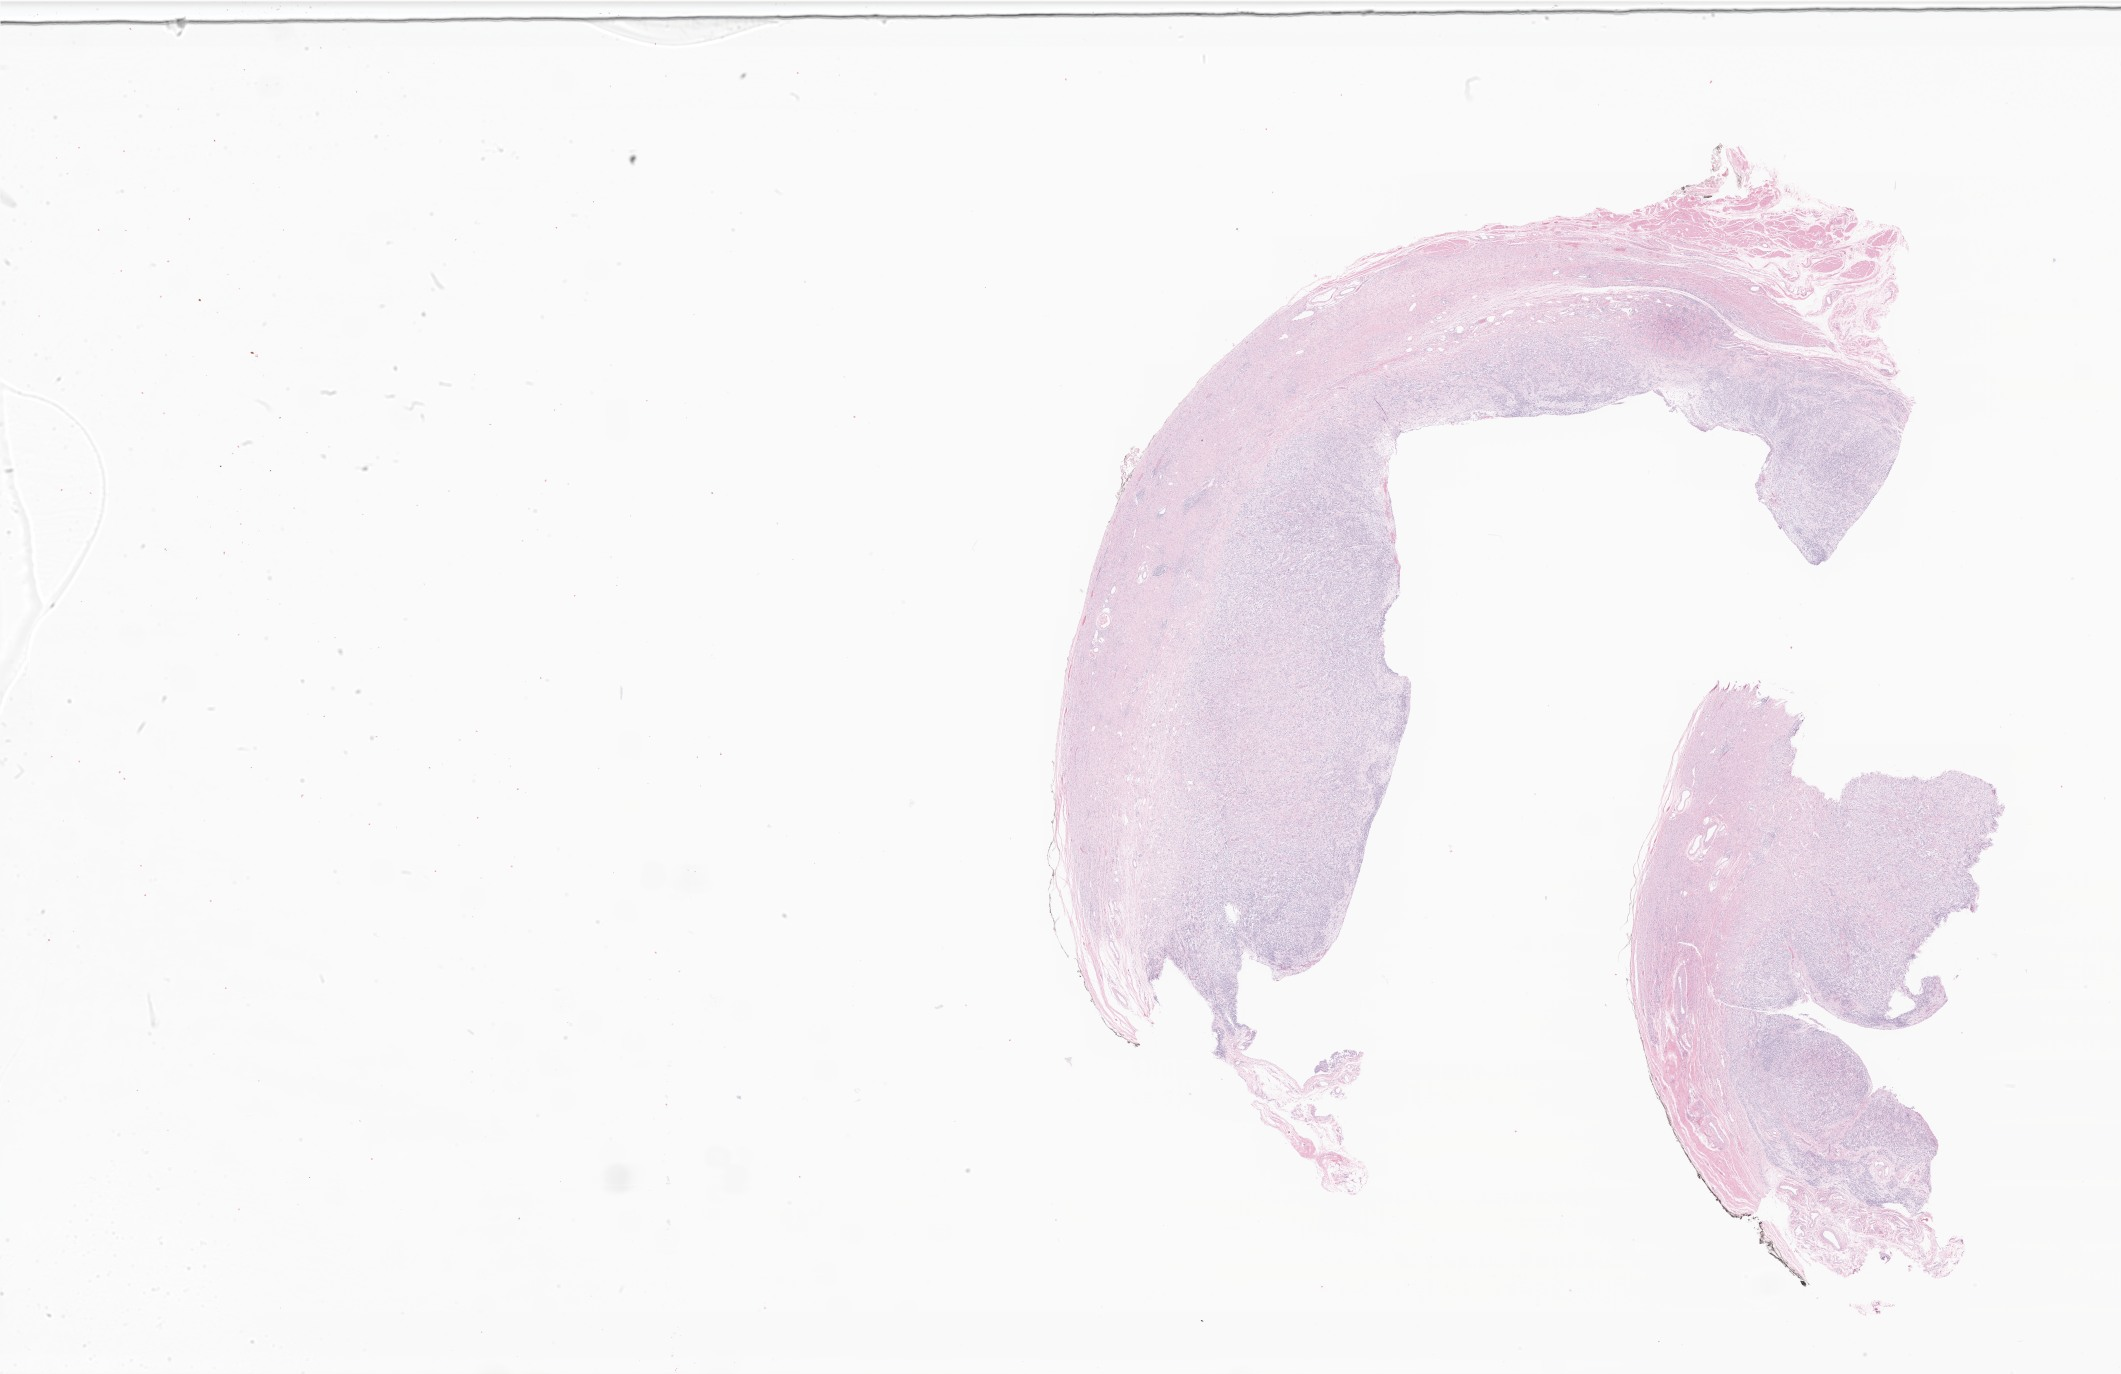
Digitized haematoxylin and eosin-stained section of tumor tissue from the testis — whole scanned area (about 35.8 x 23.2 mm) shown as a low-resolution overview; formalin-fixed paraffin-embedded section. Patient: male, age 41 months (3 years 5 months).
Diagnosis: Spindle cell rhabdomyosarcoma.